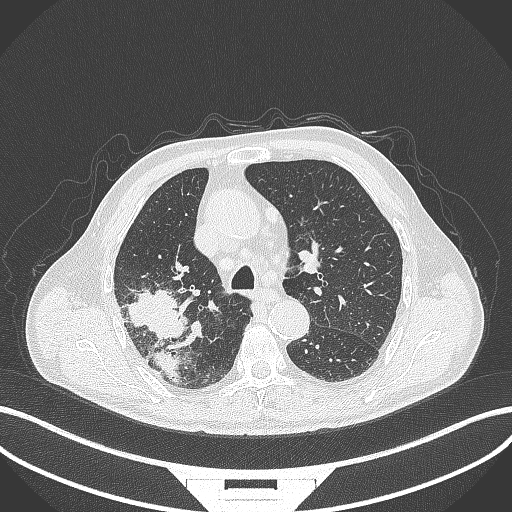
Chest CT, one axial slice; position 282 of 429 along the scan axis; 120 kVp; lung window (W 1500 / L -600 HU); 1 mm slice thickness; 512 × 512 image matrix, field of view 400 × 400 mm. Male patient, age 72 years. Case-level facts recorded for this patient, not image findings: clinical TNM (as recorded): T3 N2 M0.
Structures marked on this image (bounding box drawn by a radiologist):
- lung tumour (recorded histology: adenocarcinoma): bounding box (x1, y1, x2, y2) in pixels: (119, 280, 196, 387)